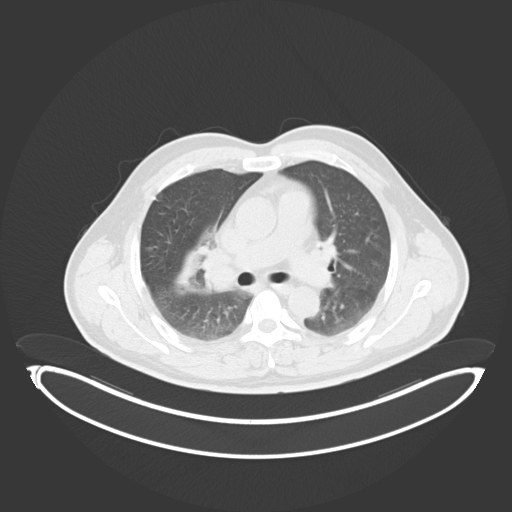
Chest CT, one axial slice. Slice 212 of 284 in the series (ordered by position). Reconstruction kernel B30f. 120 kVp. Lung window (W 1500 / L -600 HU). 512 × 512 image matrix, field of view 500 × 500 mm. Patient: male, 55 years. From the clinical record (not read from this slice): clinical TNM (as recorded): T3 N2 M1.
Structures marked on this image (rectangle marked by the reading radiologist):
- lung tumour (recorded histology: adenocarcinoma): bounding box [x1, y1, x2, y2] px = [174, 241, 203, 293]